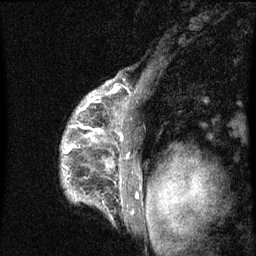
Breast MRI (dynamic contrast-enhanced), one sagittal slice; position 51 of 60 along the scan axis; dynamic contrast-enhanced series, image 2 of 3 at this slice position (ordered by acquisition); 1.5 T; TE 4.2 ms, TR 8 ms; 256 × 256 image matrix. Patient: female, 50 years.
Structures marked on this image (semi-automatic segmentation, software-assisted and operator-edited):
- analysis volume of interest (the breast-tissue region the enhancement analysis was run in; not a lesion): bounding box (x1, y1, x2, y2) in pixels: (61, 90, 142, 216)
- tumour enhancement mask (voxels above the 70 % enhancement threshold inside the analysis volume of interest): (64, 92, 122, 178)